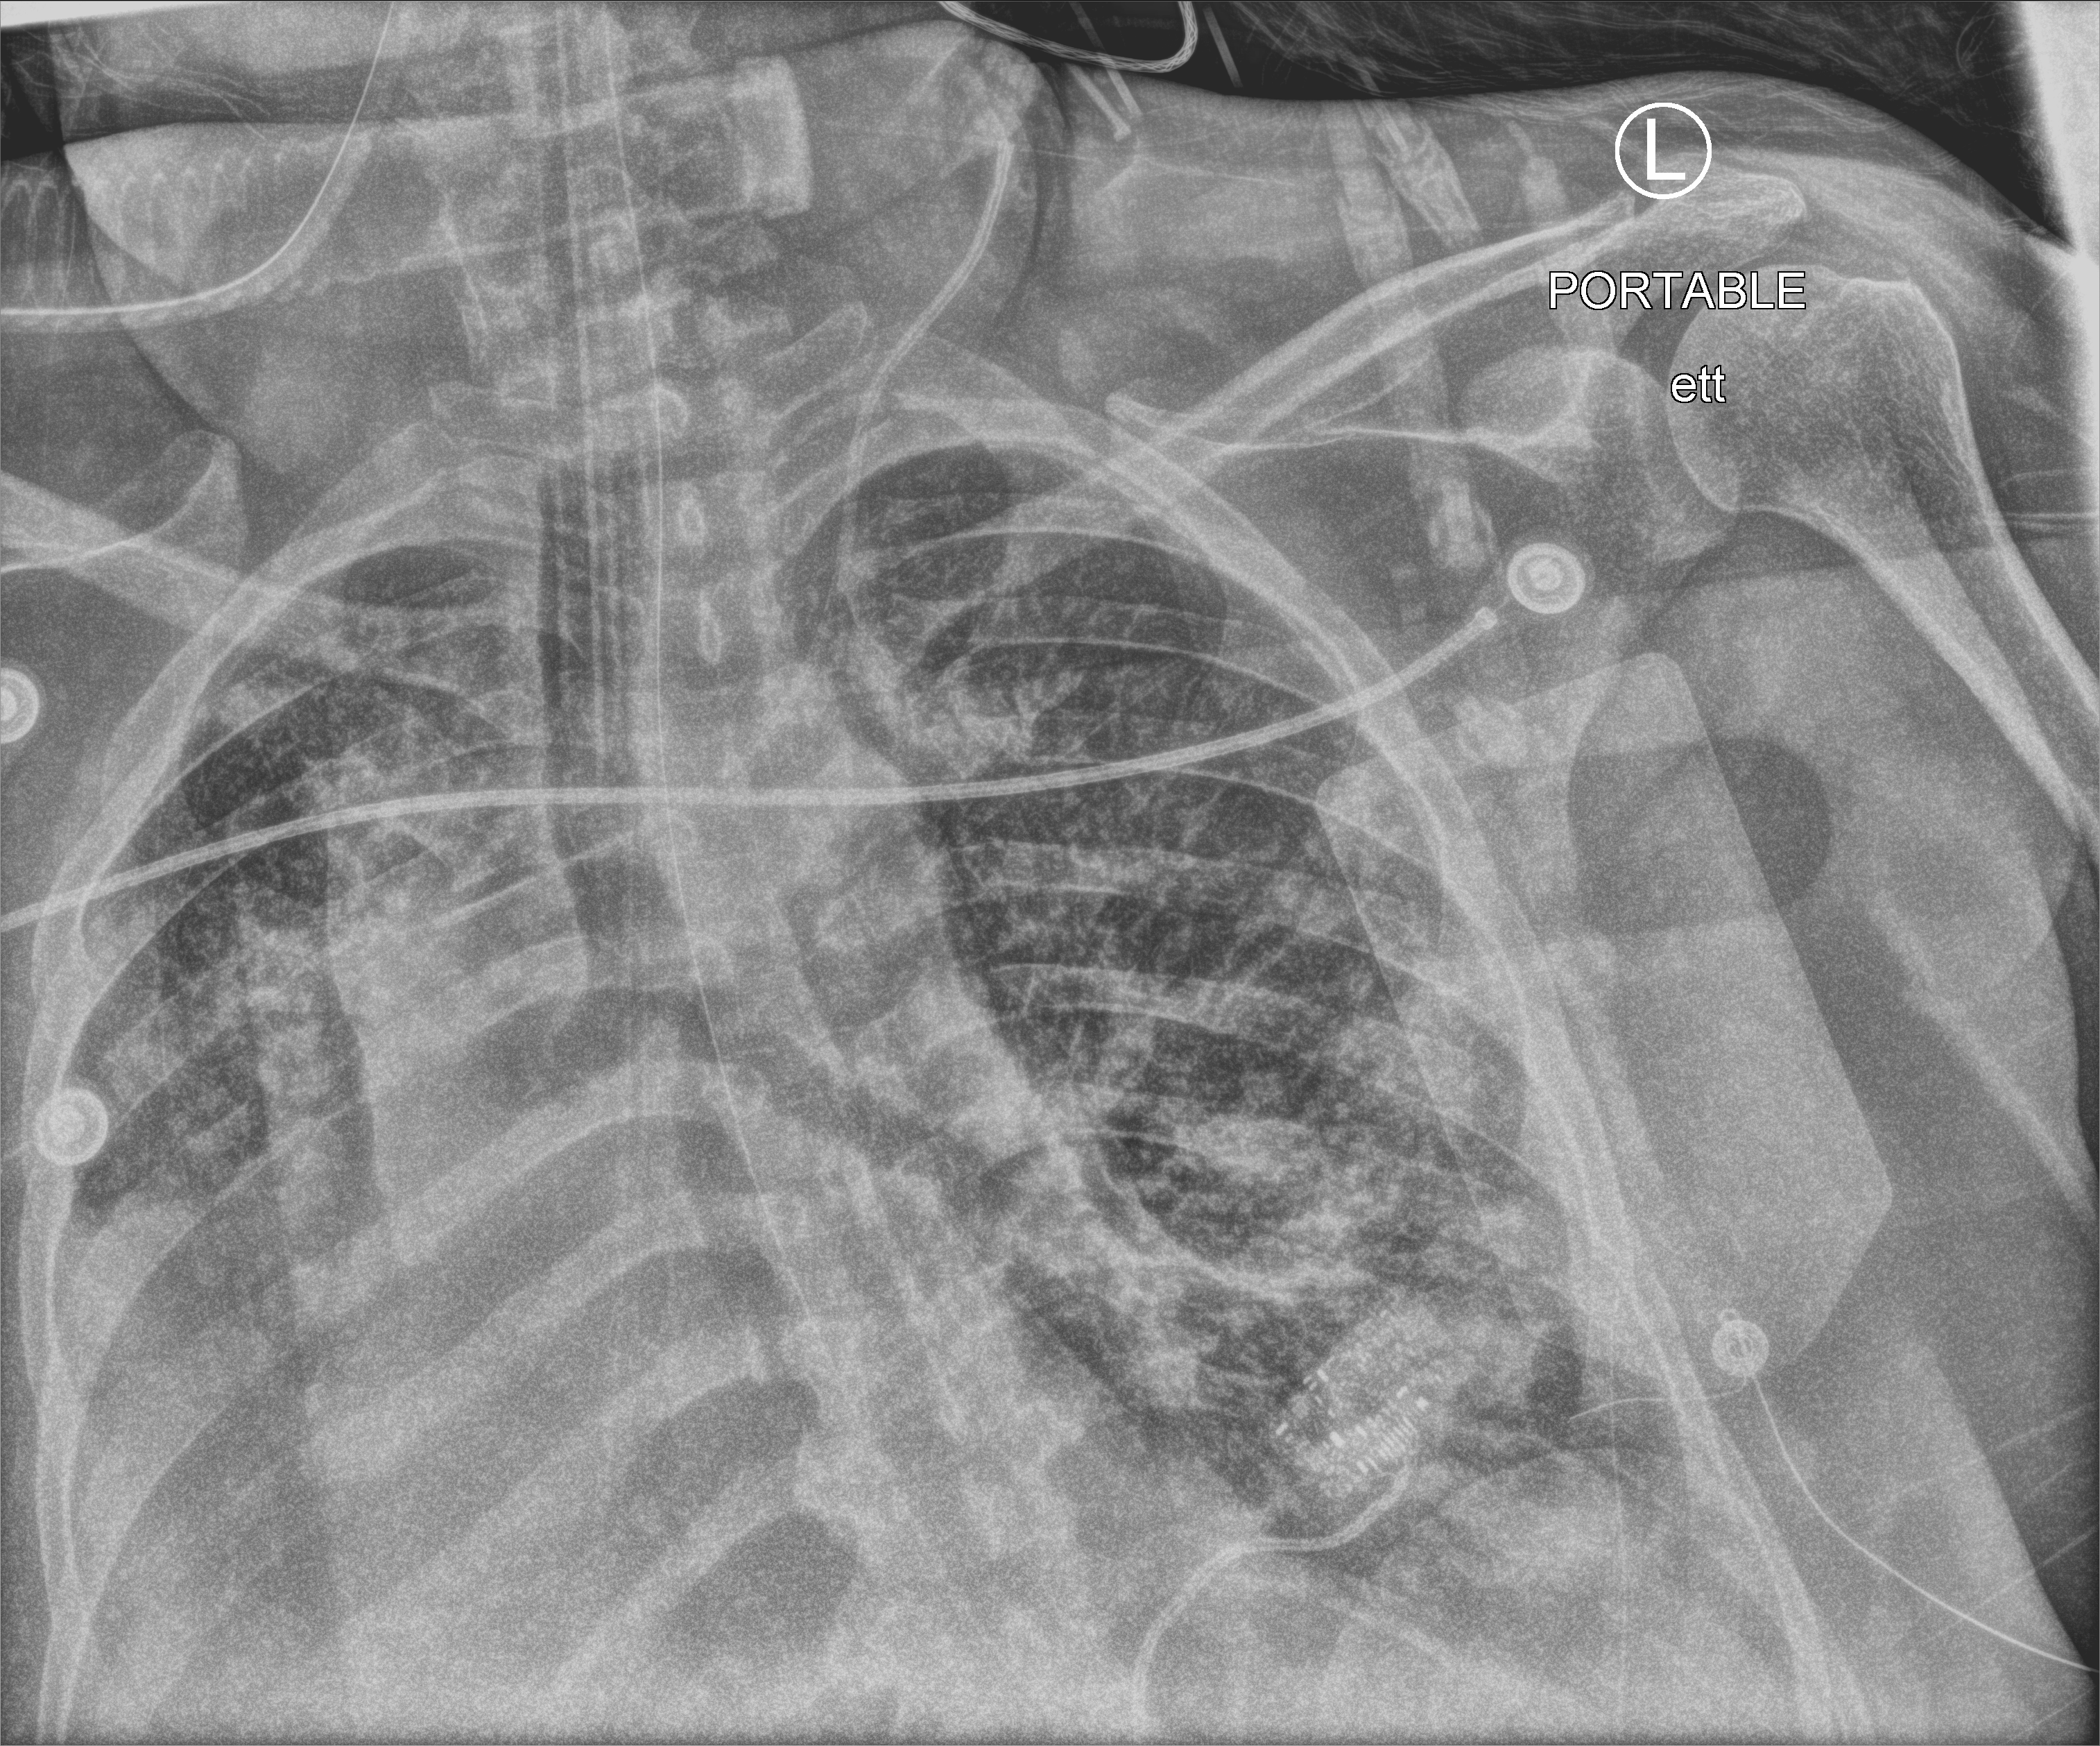
Bedside chest radiograph (computed radiography). Adult patient hospitalised with COVID-19, age 18–59 years.
From the hospital-stay record, not from the radiograph (when in the stay this image was taken is not recorded):
- hypertension (admission record): yes
- mechanically ventilated during this hospital stay: yes
- smoking status (admission record): never